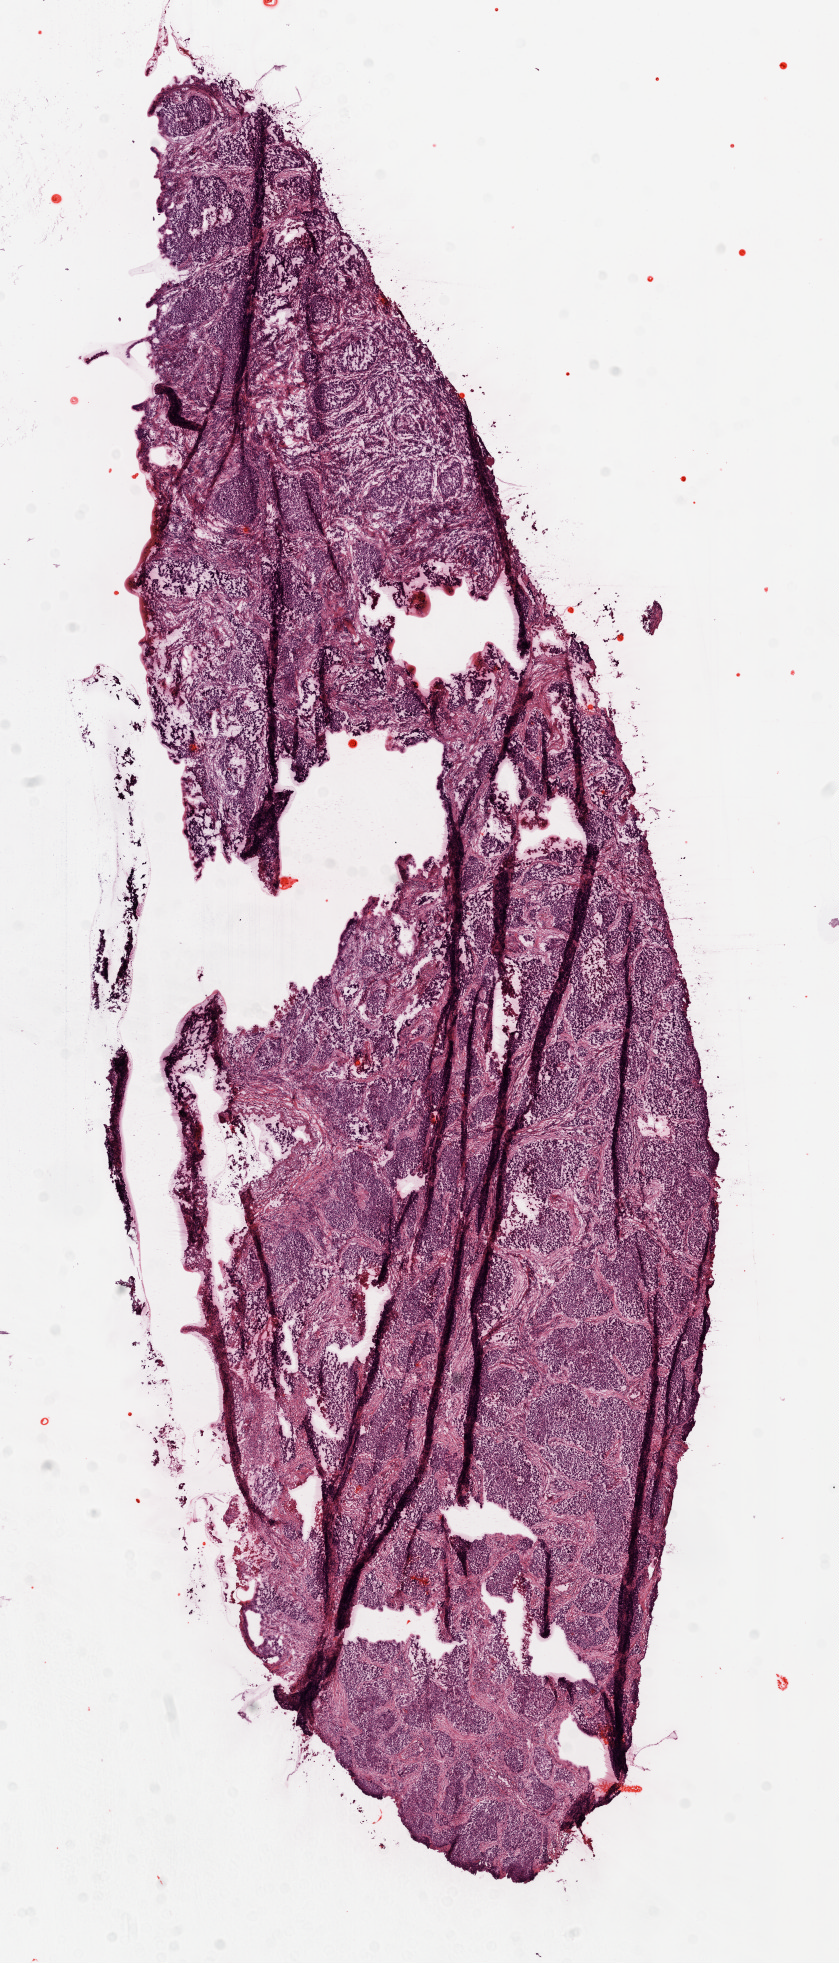
H&E-stained whole-slide image, a low-resolution overview of the entire scanned area, about 6.8 x 15.8 mm (from a 20x scan), frozen section from the top of the tissue portion, sample: primary tumour, lung. Patient: male, age at initial diagnosis 75 years.
Pathologic diagnosis: Squamous cell carcinoma, NOS (upper lobe, lung).